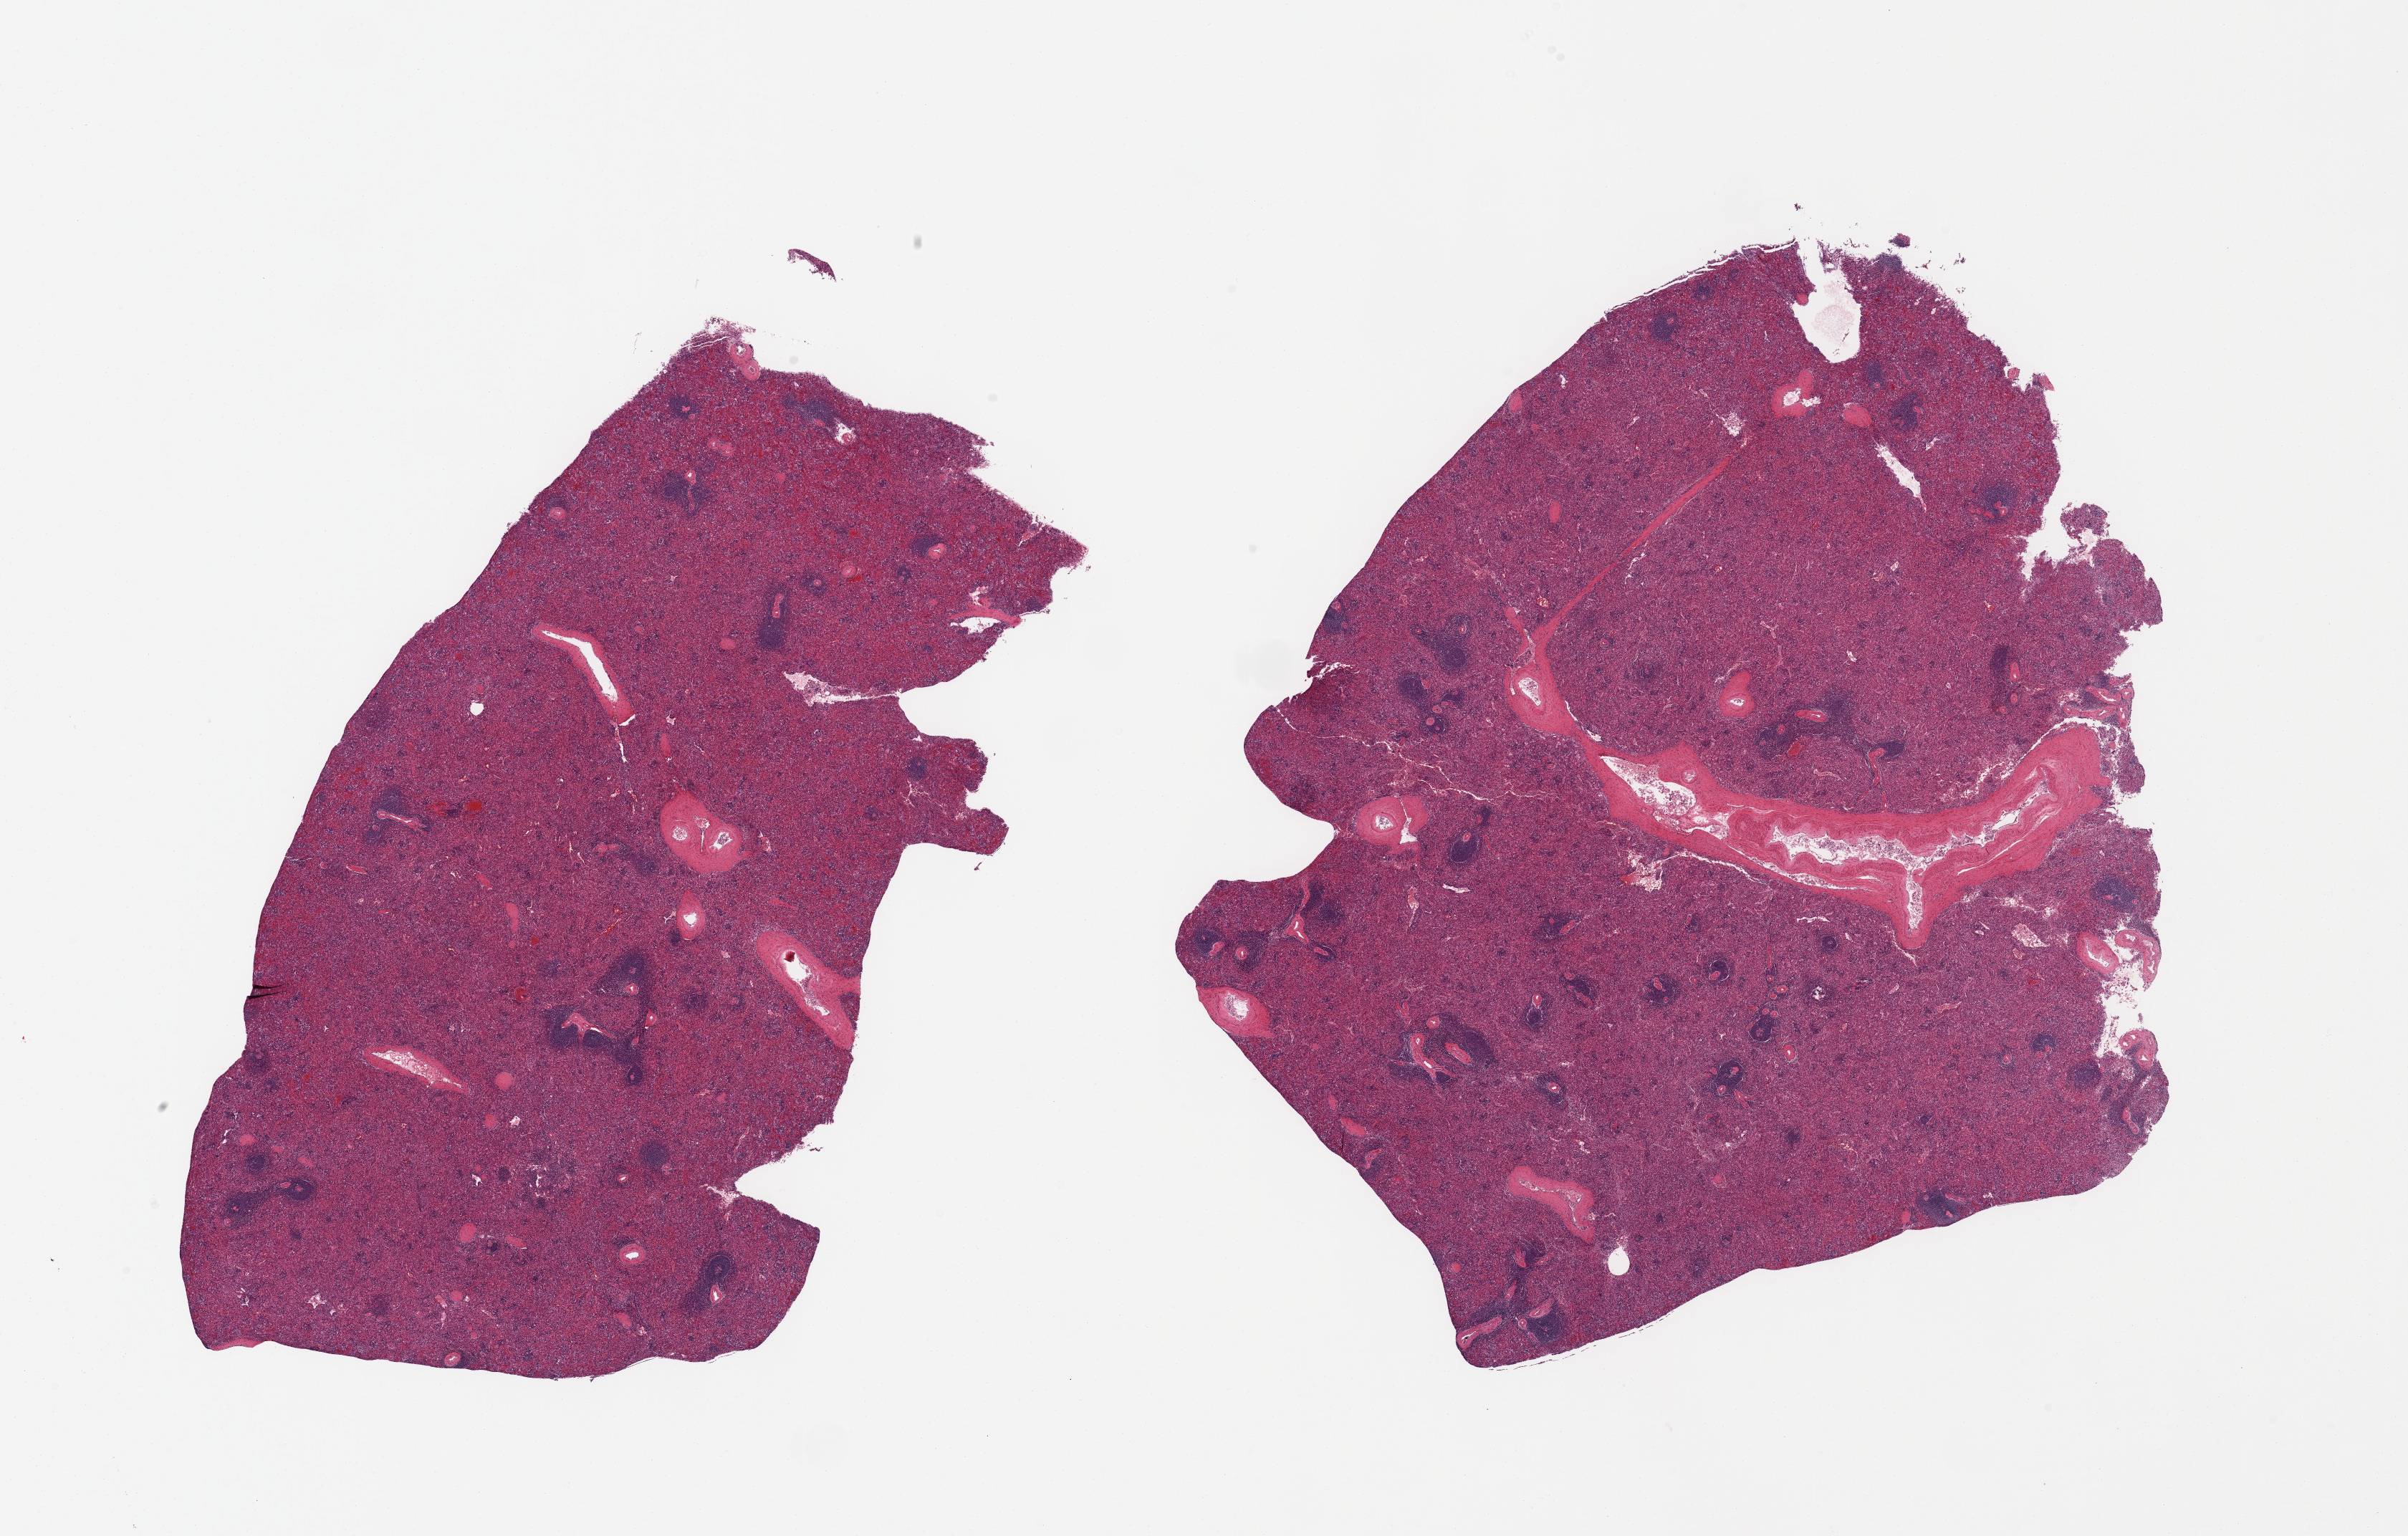
Digitized haematoxylin and eosin-stained section, brightfield — low-resolution overview of the scanned area, about 26.6 x 17.0 mm (slide scanned at 20x); PAXgene-fixed, paraffin-embedded tissue; target tissue: spleen; tissue donor sample. Donor sex: female.
Pathologist's review note for this sample: 2 pieces; mild congestion; numerous foamy macrophages lining sinusoids.